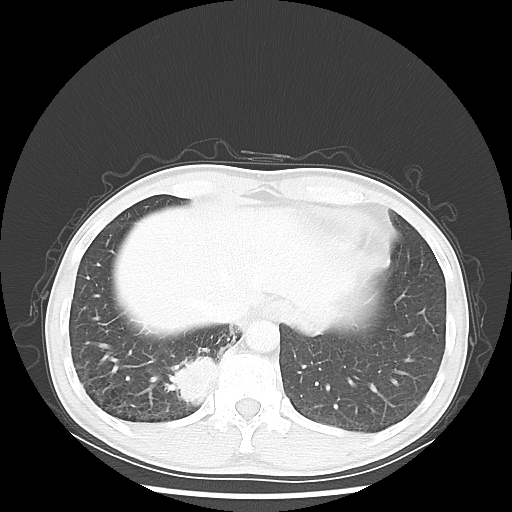
Chest CT, one axial slice; position 9 of 58 along the scan axis; 100 kVp; lung window (W 1500 / L -600 HU); 5 mm slice thickness; 512 × 512 image matrix. Patient: male, 56 years. Case-level facts recorded for this patient, not image findings: clinical TNM (as recorded): T2 N1 M1; histopathological grade: G1.
Structures marked on this image (bounding box drawn by a radiologist):
- lung tumour (recorded histology: adenocarcinoma): bounding box [x1, y1, x2, y2] px = [164, 353, 219, 409]